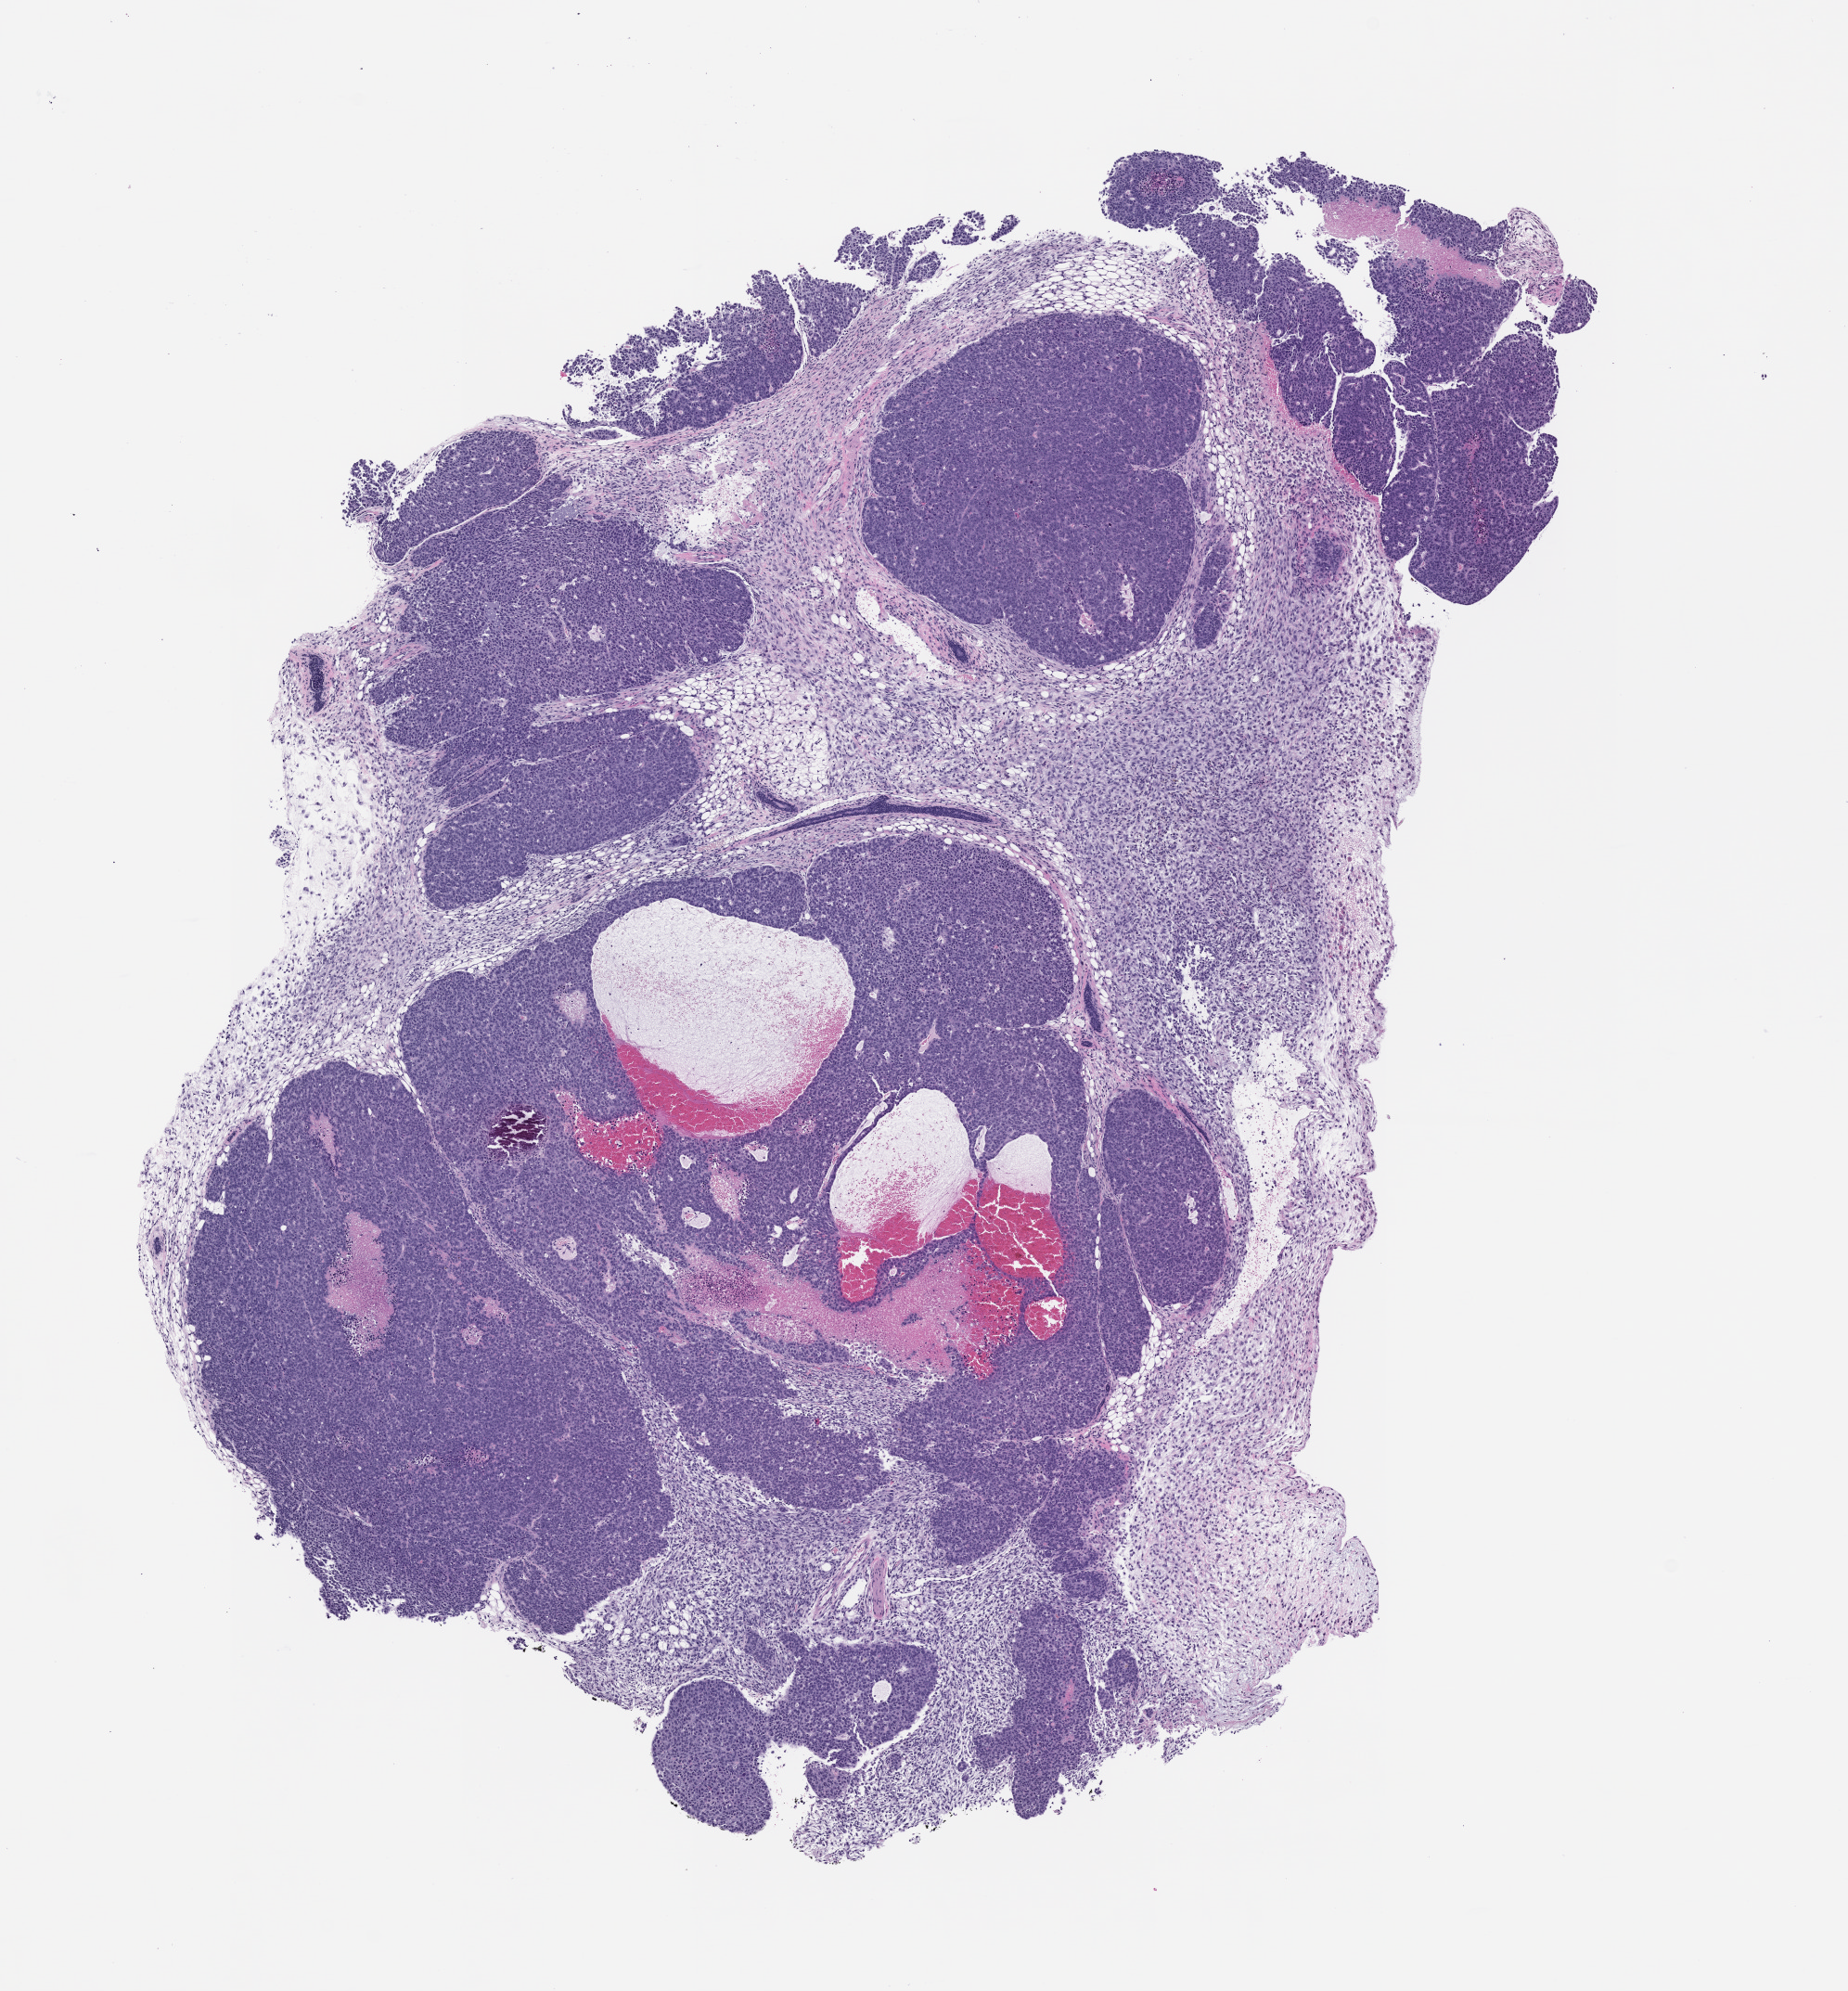
Whole-slide image, hematoxylin and eosin (H&E): patient-derived xenograft (human tumor grown in a mouse), passage 1, shown as a low-resolution overview of the whole scanned area (about 8.0 x 8.6 mm); formalin-fixed paraffin-embedded section; originating tumor site category: colon.
• originating patient diagnosis: Colon Adenocarcinoma